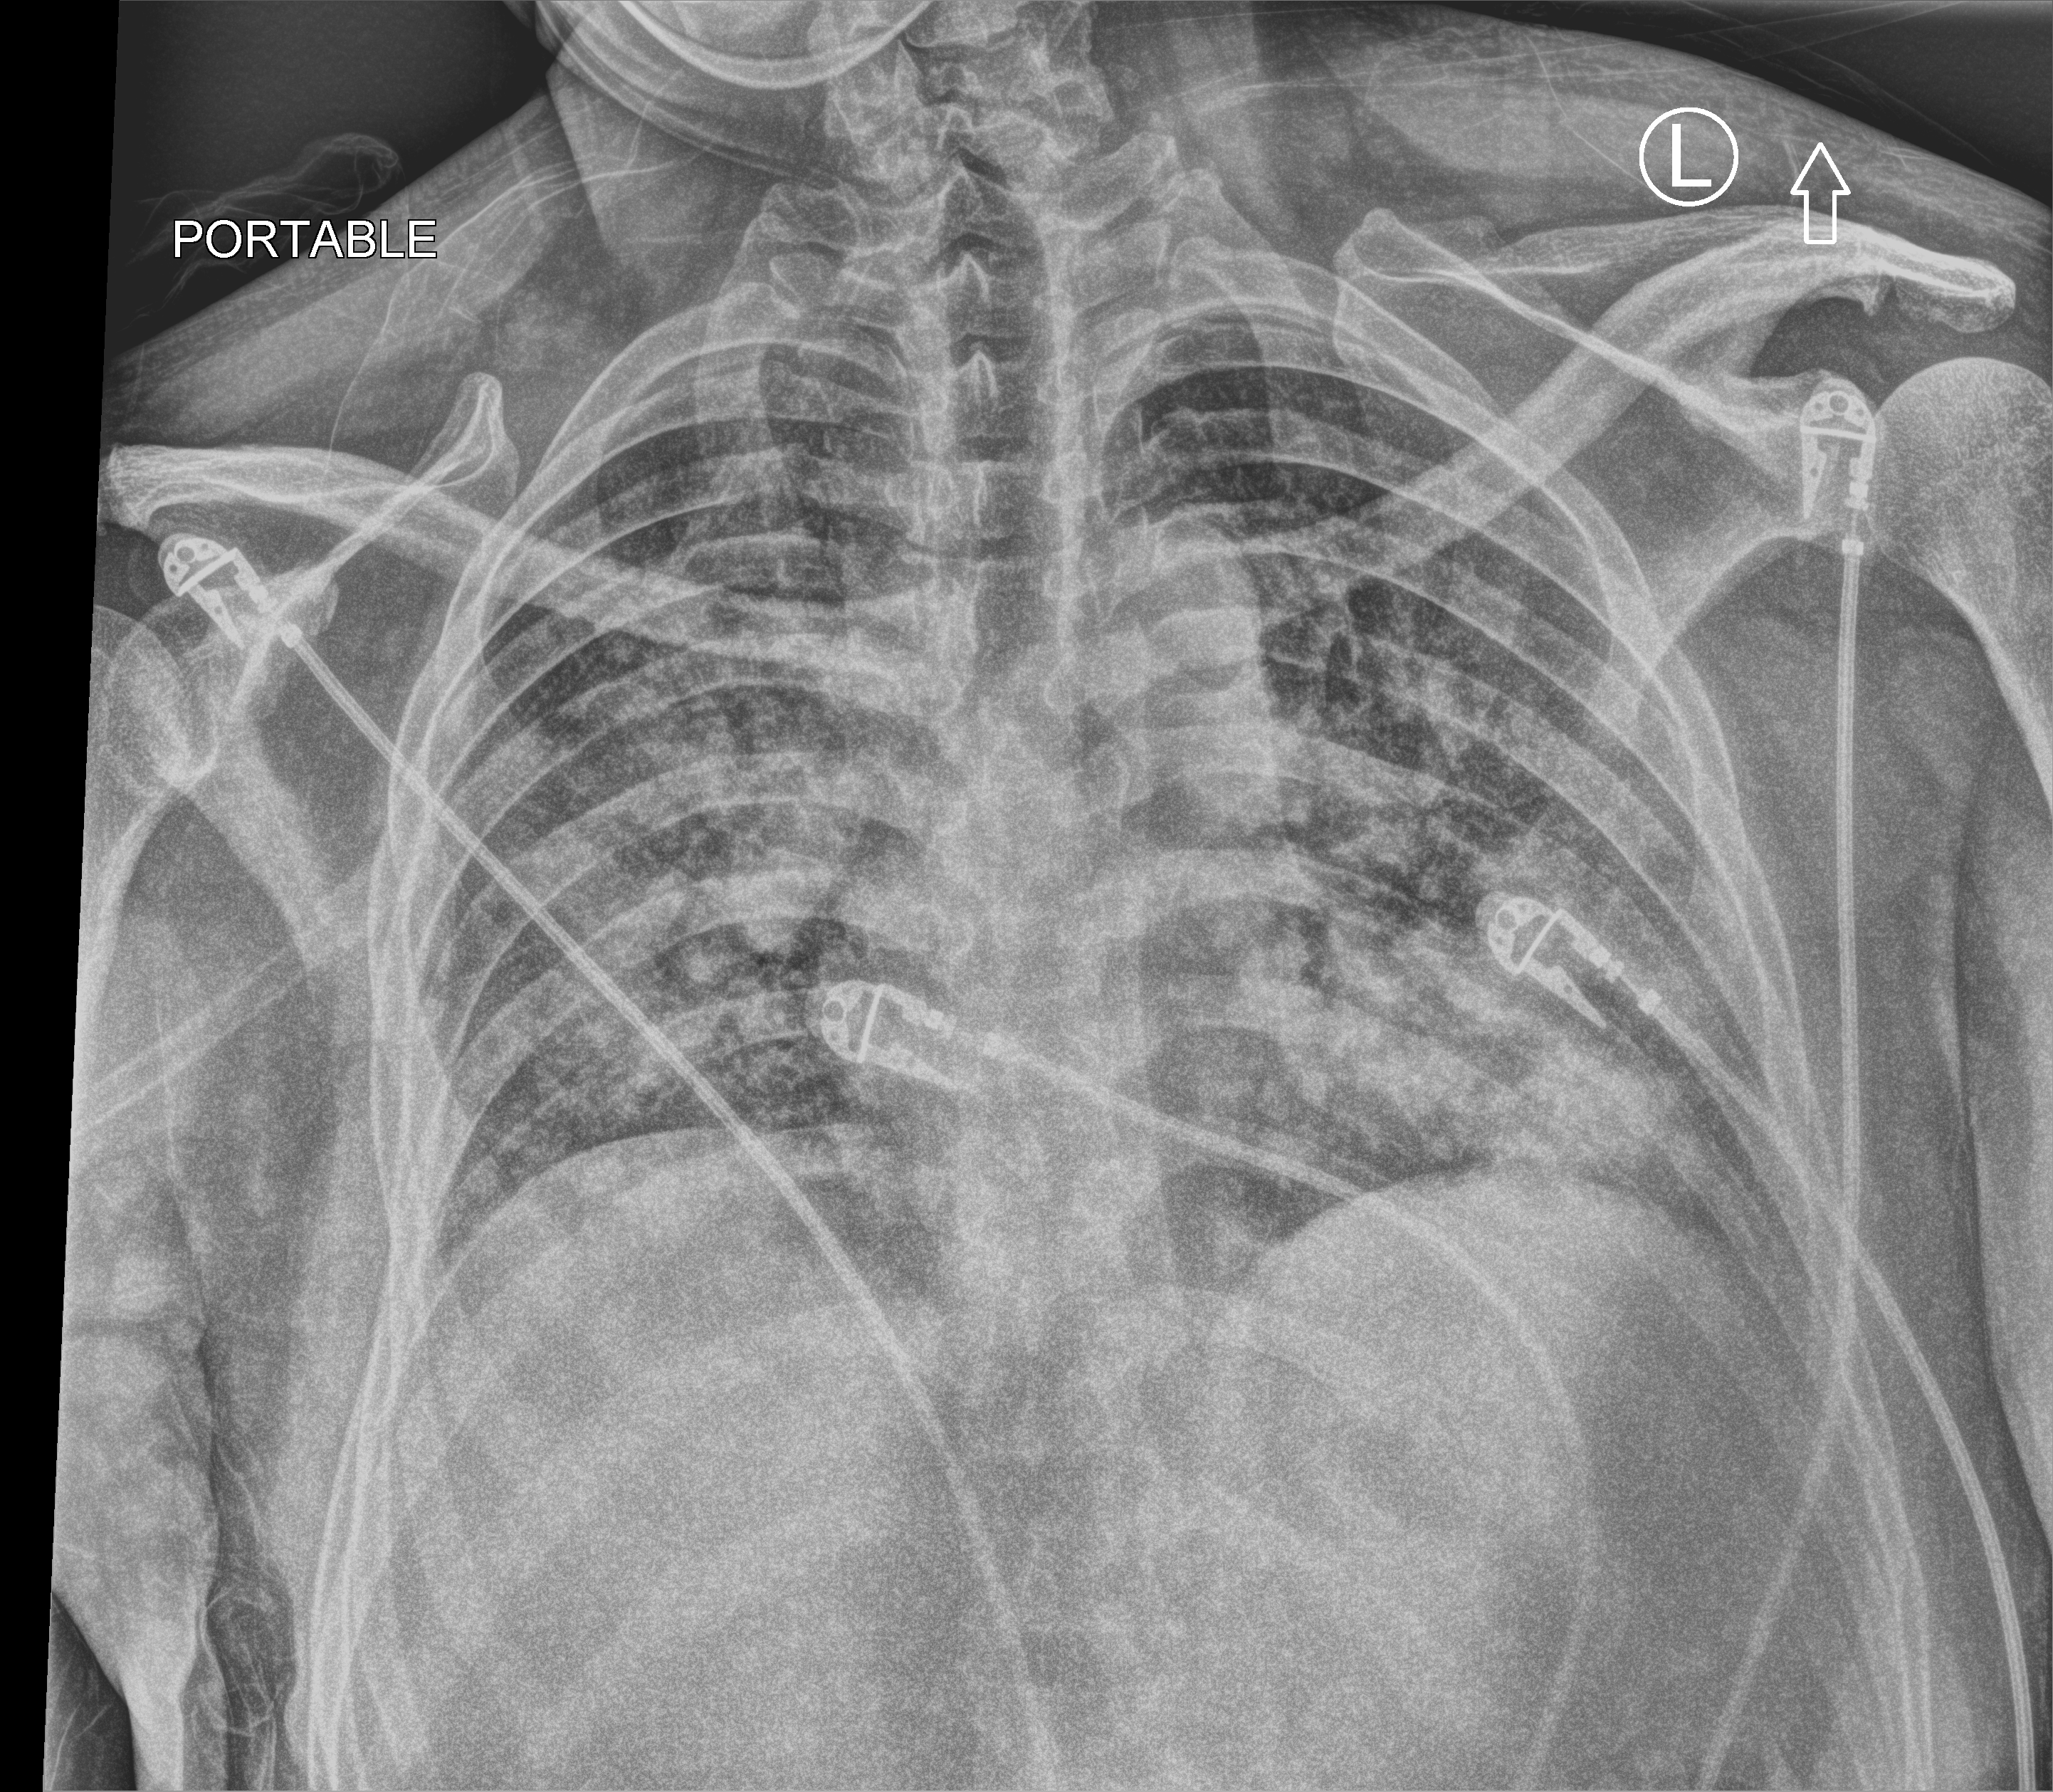
Bedside chest radiograph (computed radiography), anteroposterior (AP) projection. Male patient hospitalised with COVID-19, age 18–59 years.
Hospital-stay facts (about this admission, not read from this image; timing relative to this image not recorded): admitted to intensive care during this hospital stay: no; mechanically ventilated during this hospital stay: no; length of hospital stay: 14 days.